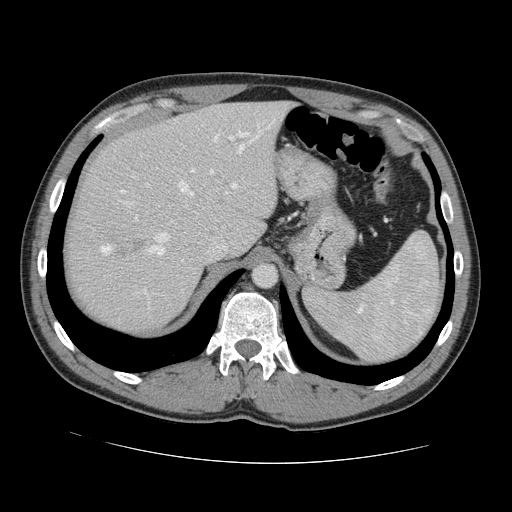
Contrast-enhanced abdominal CT, one axial slice. Slice 101 of 131 in the series (ordered by position). 120 kVp. Intravenous contrast given. Soft-tissue window (W 400 / L 40 HU). 2.5 mm slice thickness. 512 × 512 image matrix, field of view 380 × 380 mm. Male patient, age 40 years. From the clinical record (not read from this slice): diagnosis: colorectal cancer liver metastases, imaged before liver resection; multiple liver metastases: yes; largest metastasis: 2.9 cm.
Outlined on this slice (manually delineated by an expert):
- hepatic veins: bounding box <149,136,244,256> (left, top, right, bottom; pixels)
- liver: <67,102,288,332>
- planned liver remnant (the part of the liver to remain after resection): <97,102,287,253>
- portal vein (with intrahepatic branches): <191,132,250,189>
- liver metastasis: <122,243,143,253>